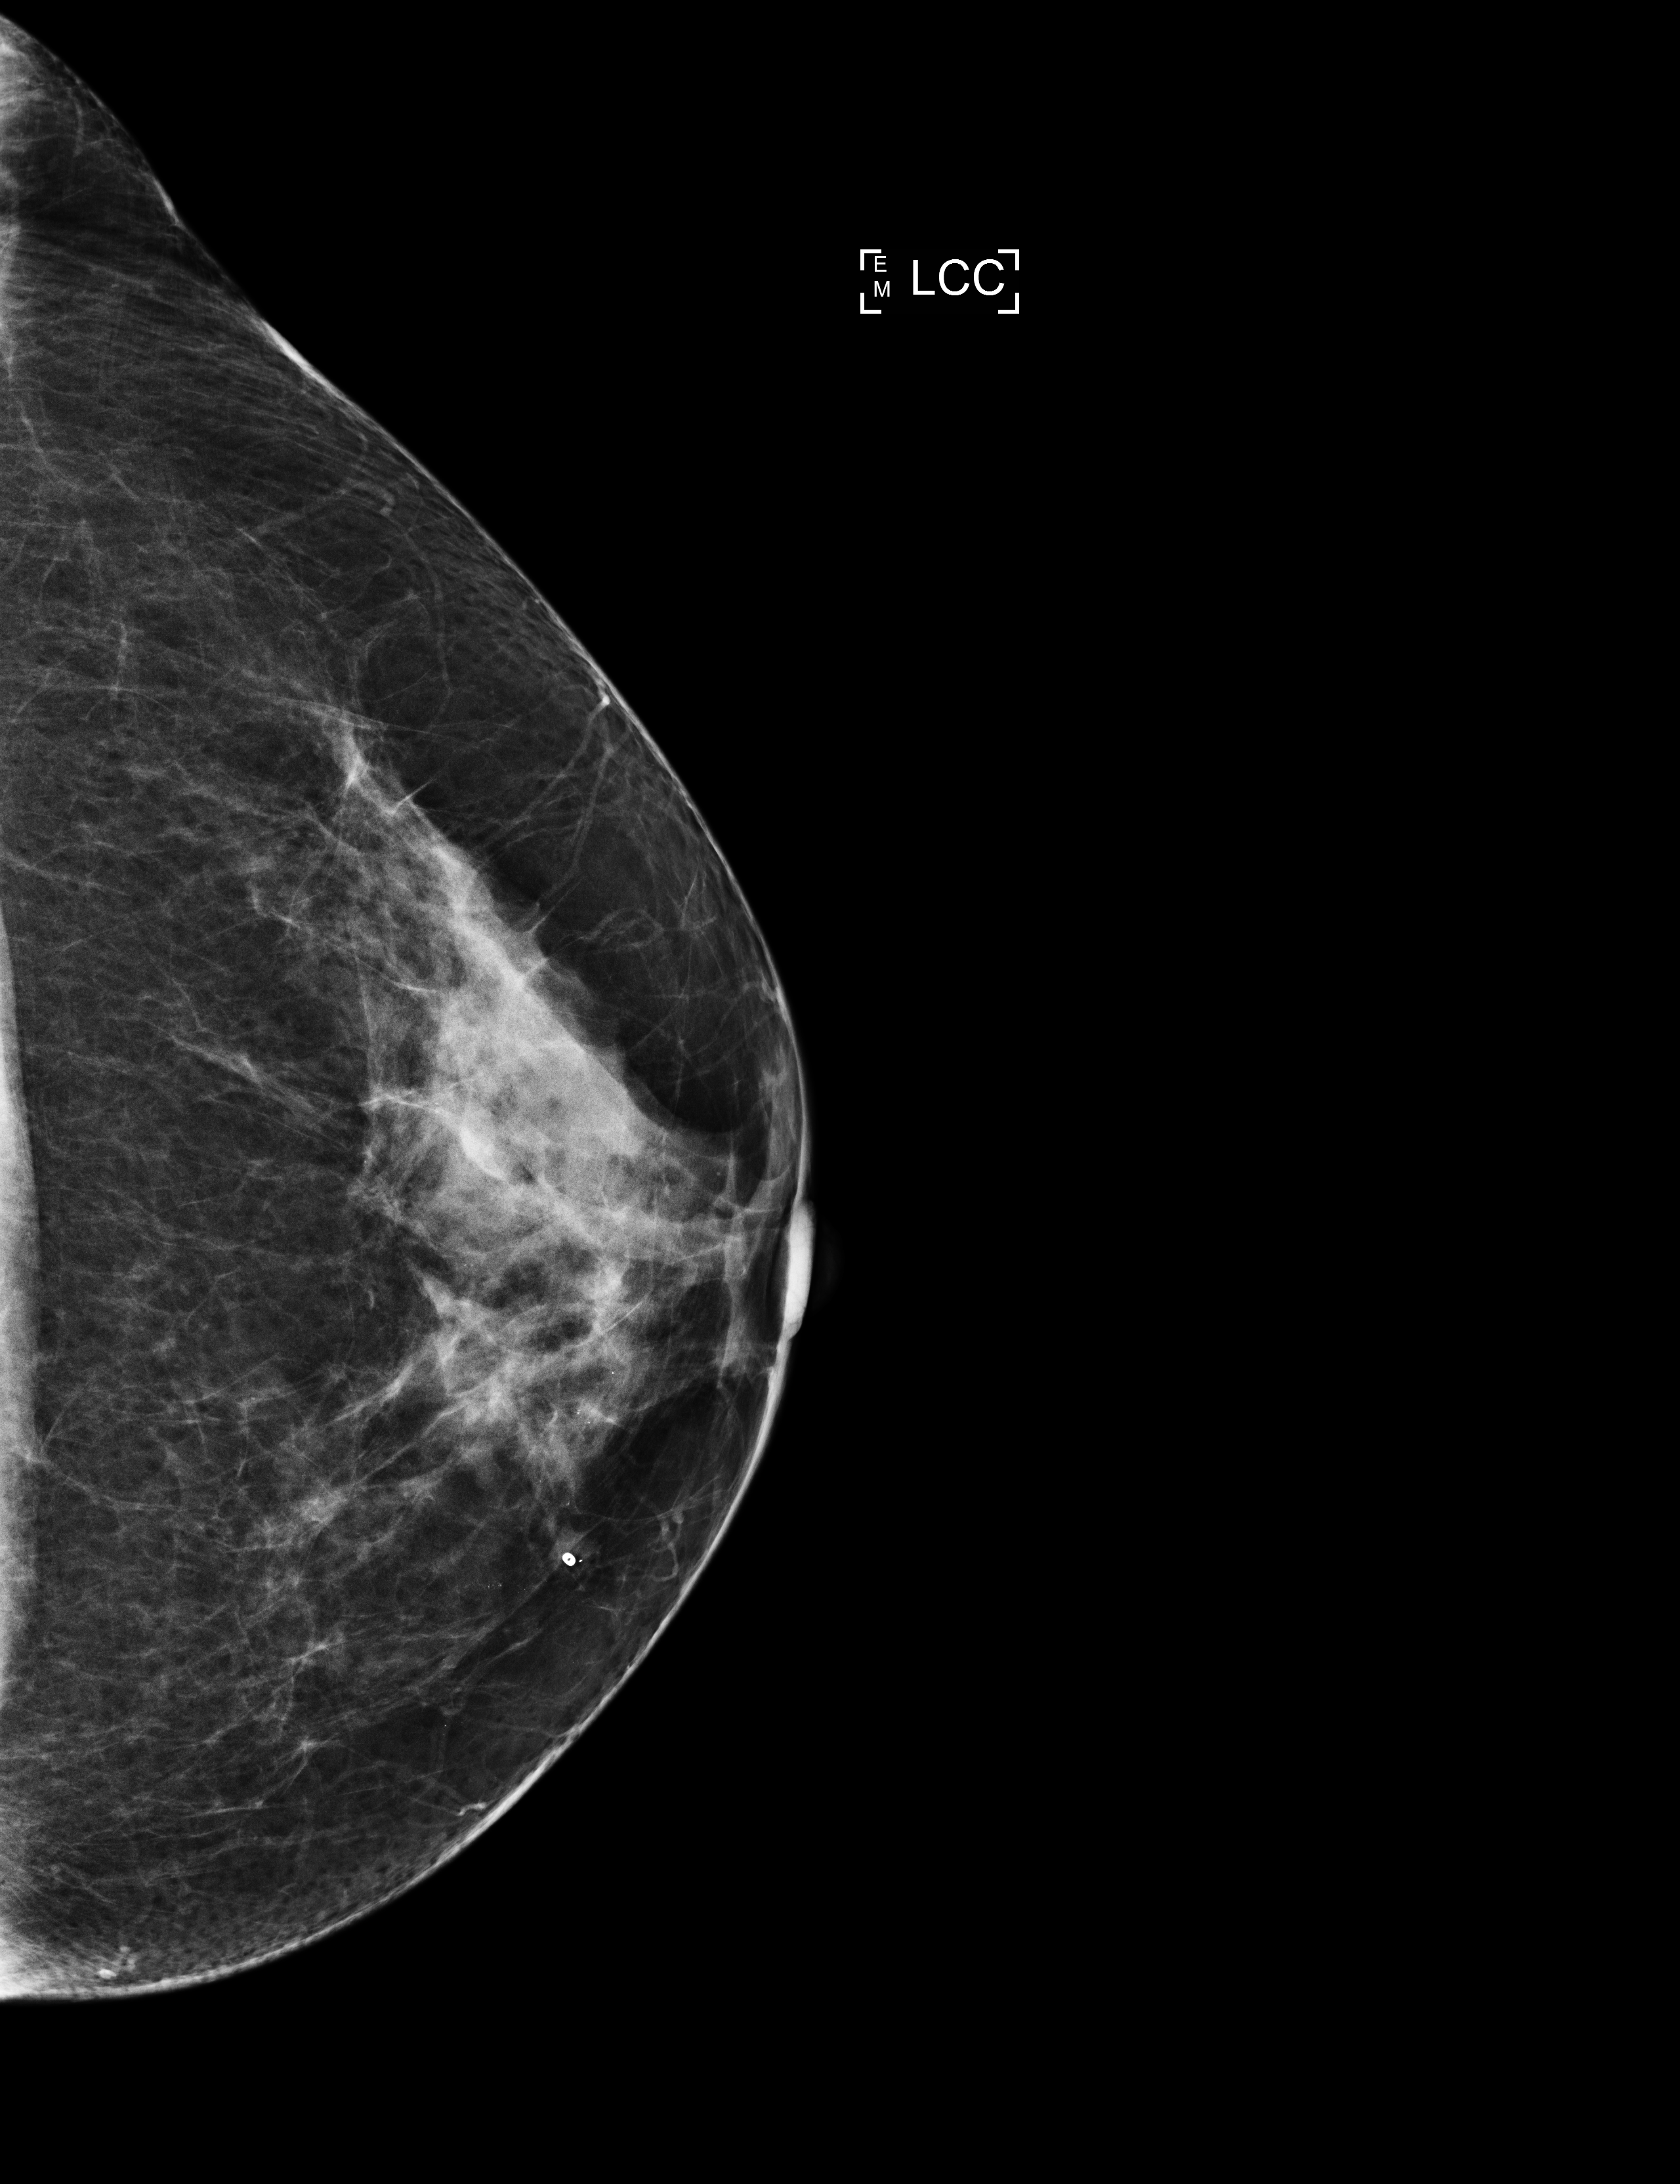
Screening examination; compressed breast thickness 62 mm; system: Selenia Dimensions. Female patient, age 57 years.
Image type: full-field digital mammogram. Breast: left. Projection: cranio-caudal projection.